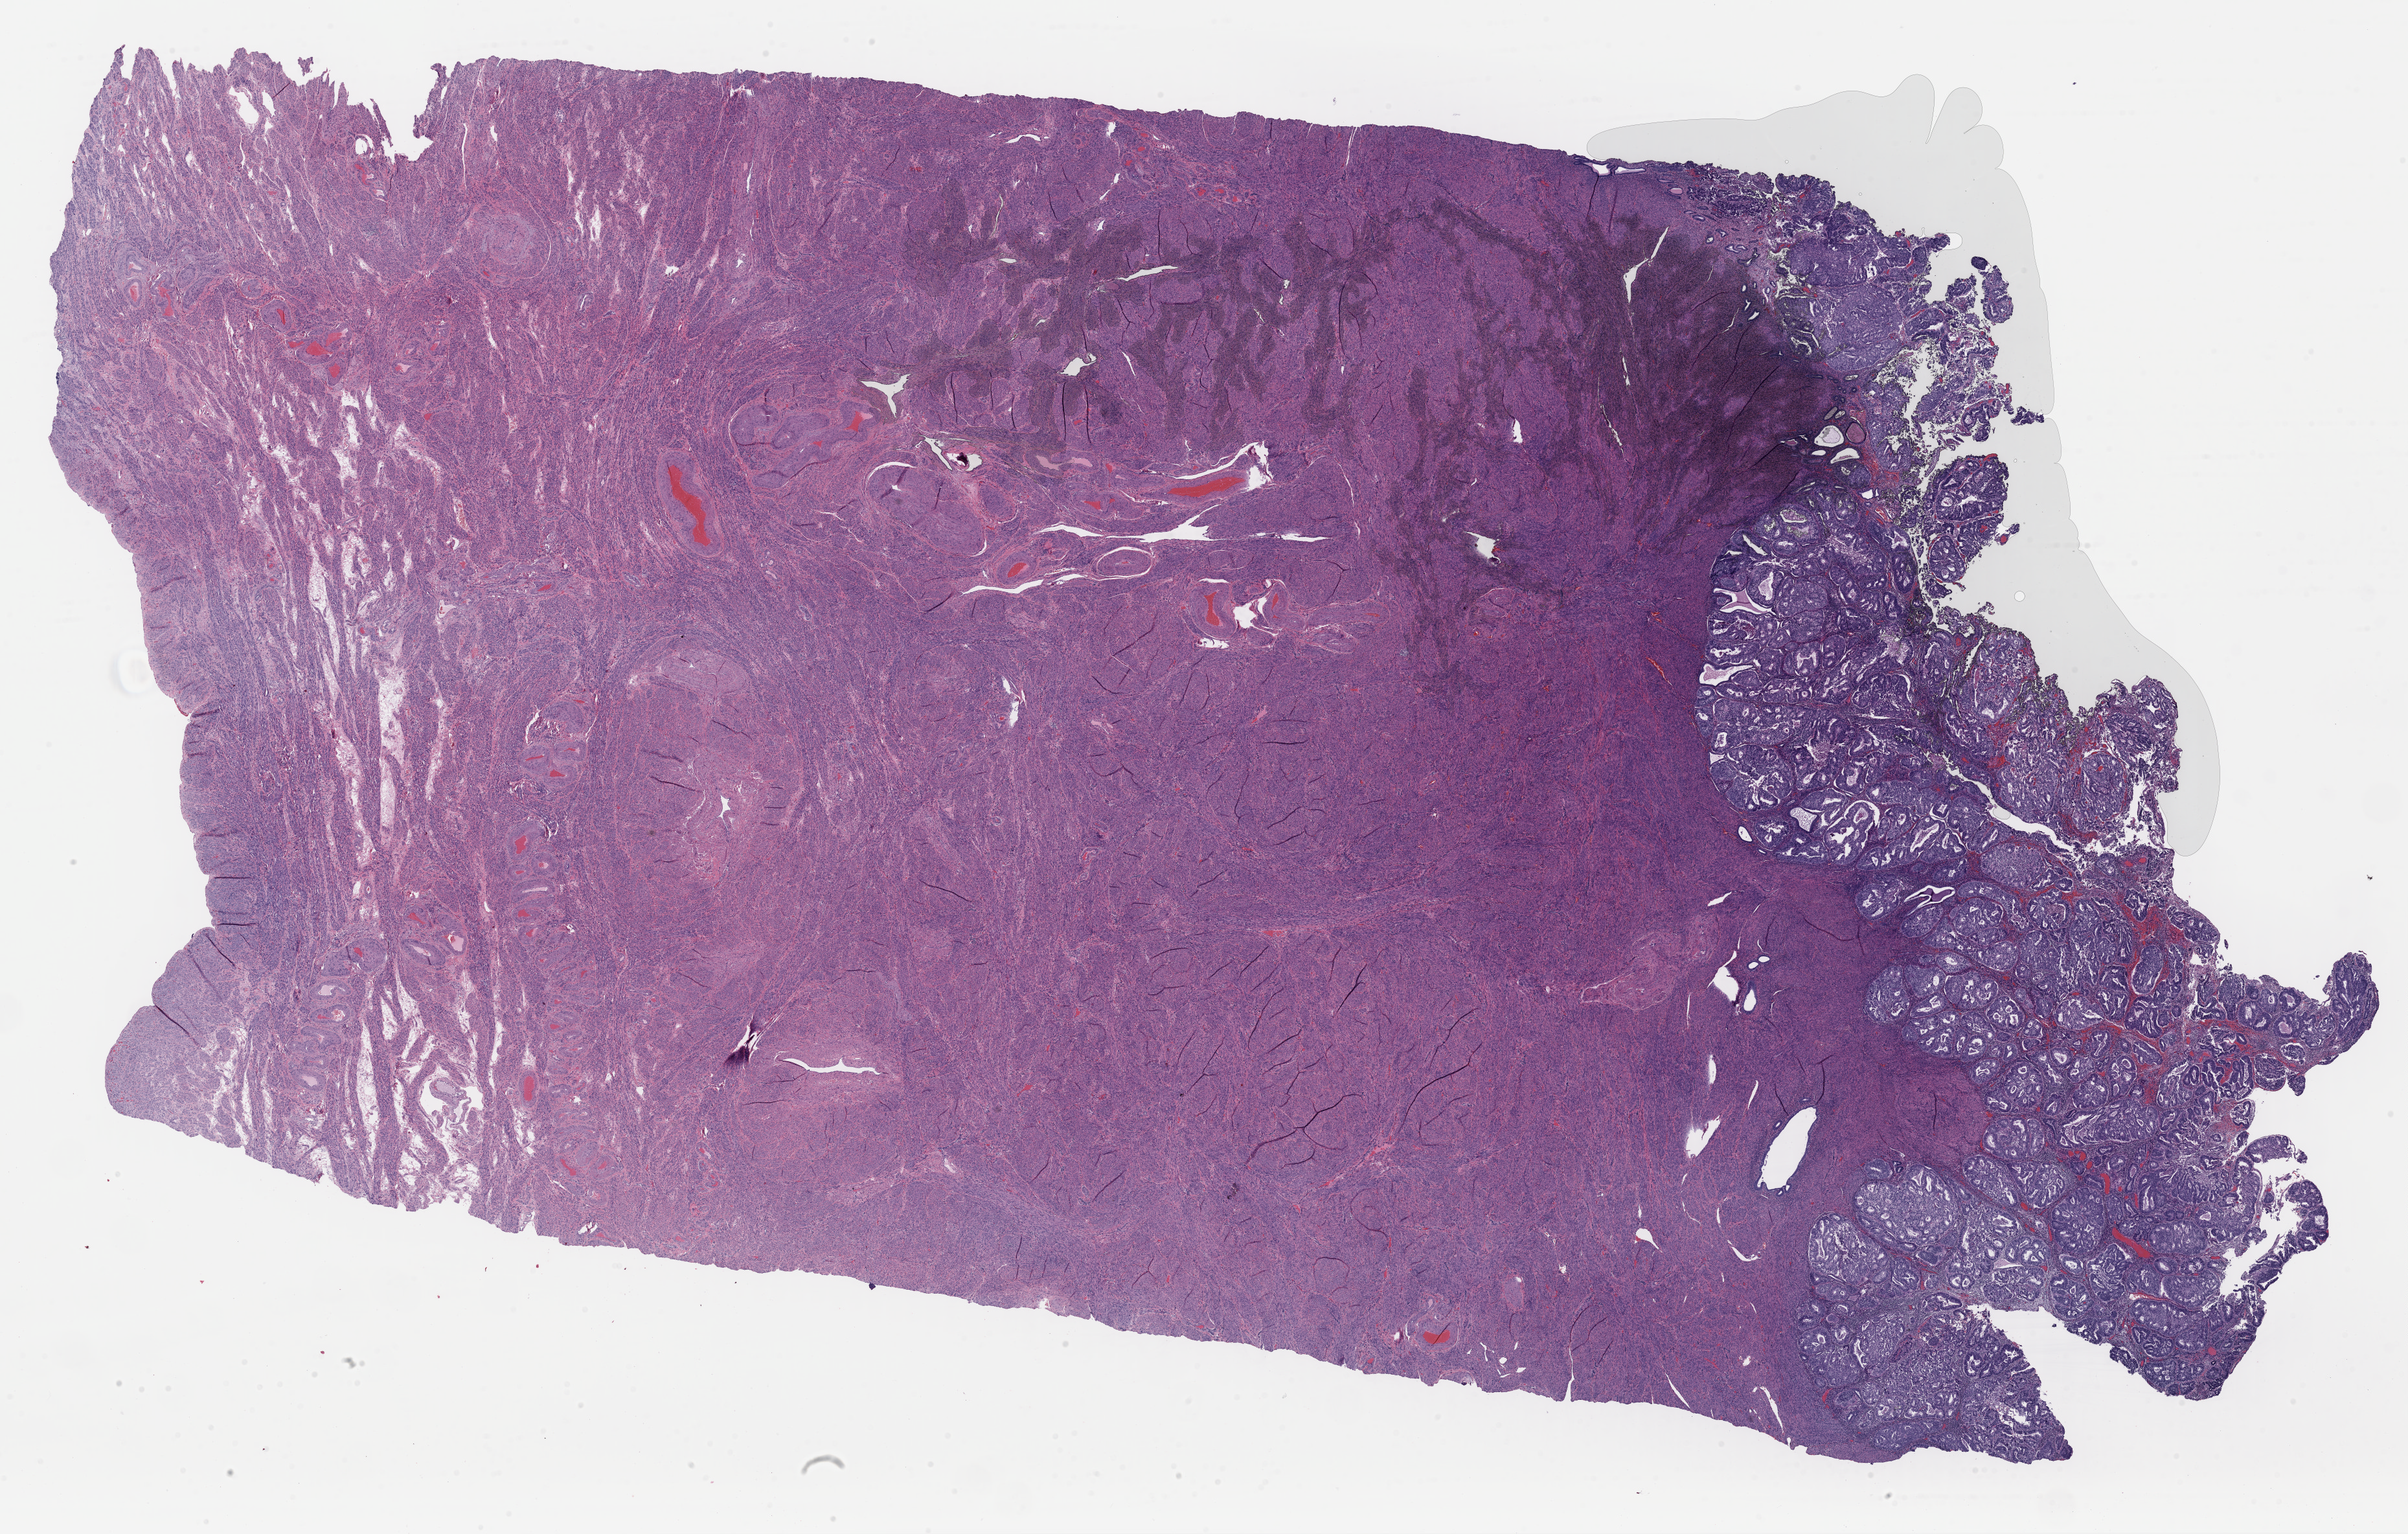
Whole-slide histology image, H&E-stained — a low-resolution overview of the entire scanned area, about 29.4 x 18.7 mm. Formalin-fixed paraffin-embedded (FFPE) diagnostic section. Uterus, primary tumour sample. Female patient; age at initial diagnosis 72 years. Histologic grade: G2 (moderately differentiated).
FIGO stage: IA. Diagnosis: Endometrioid adenocarcinoma, NOS (endometrium).